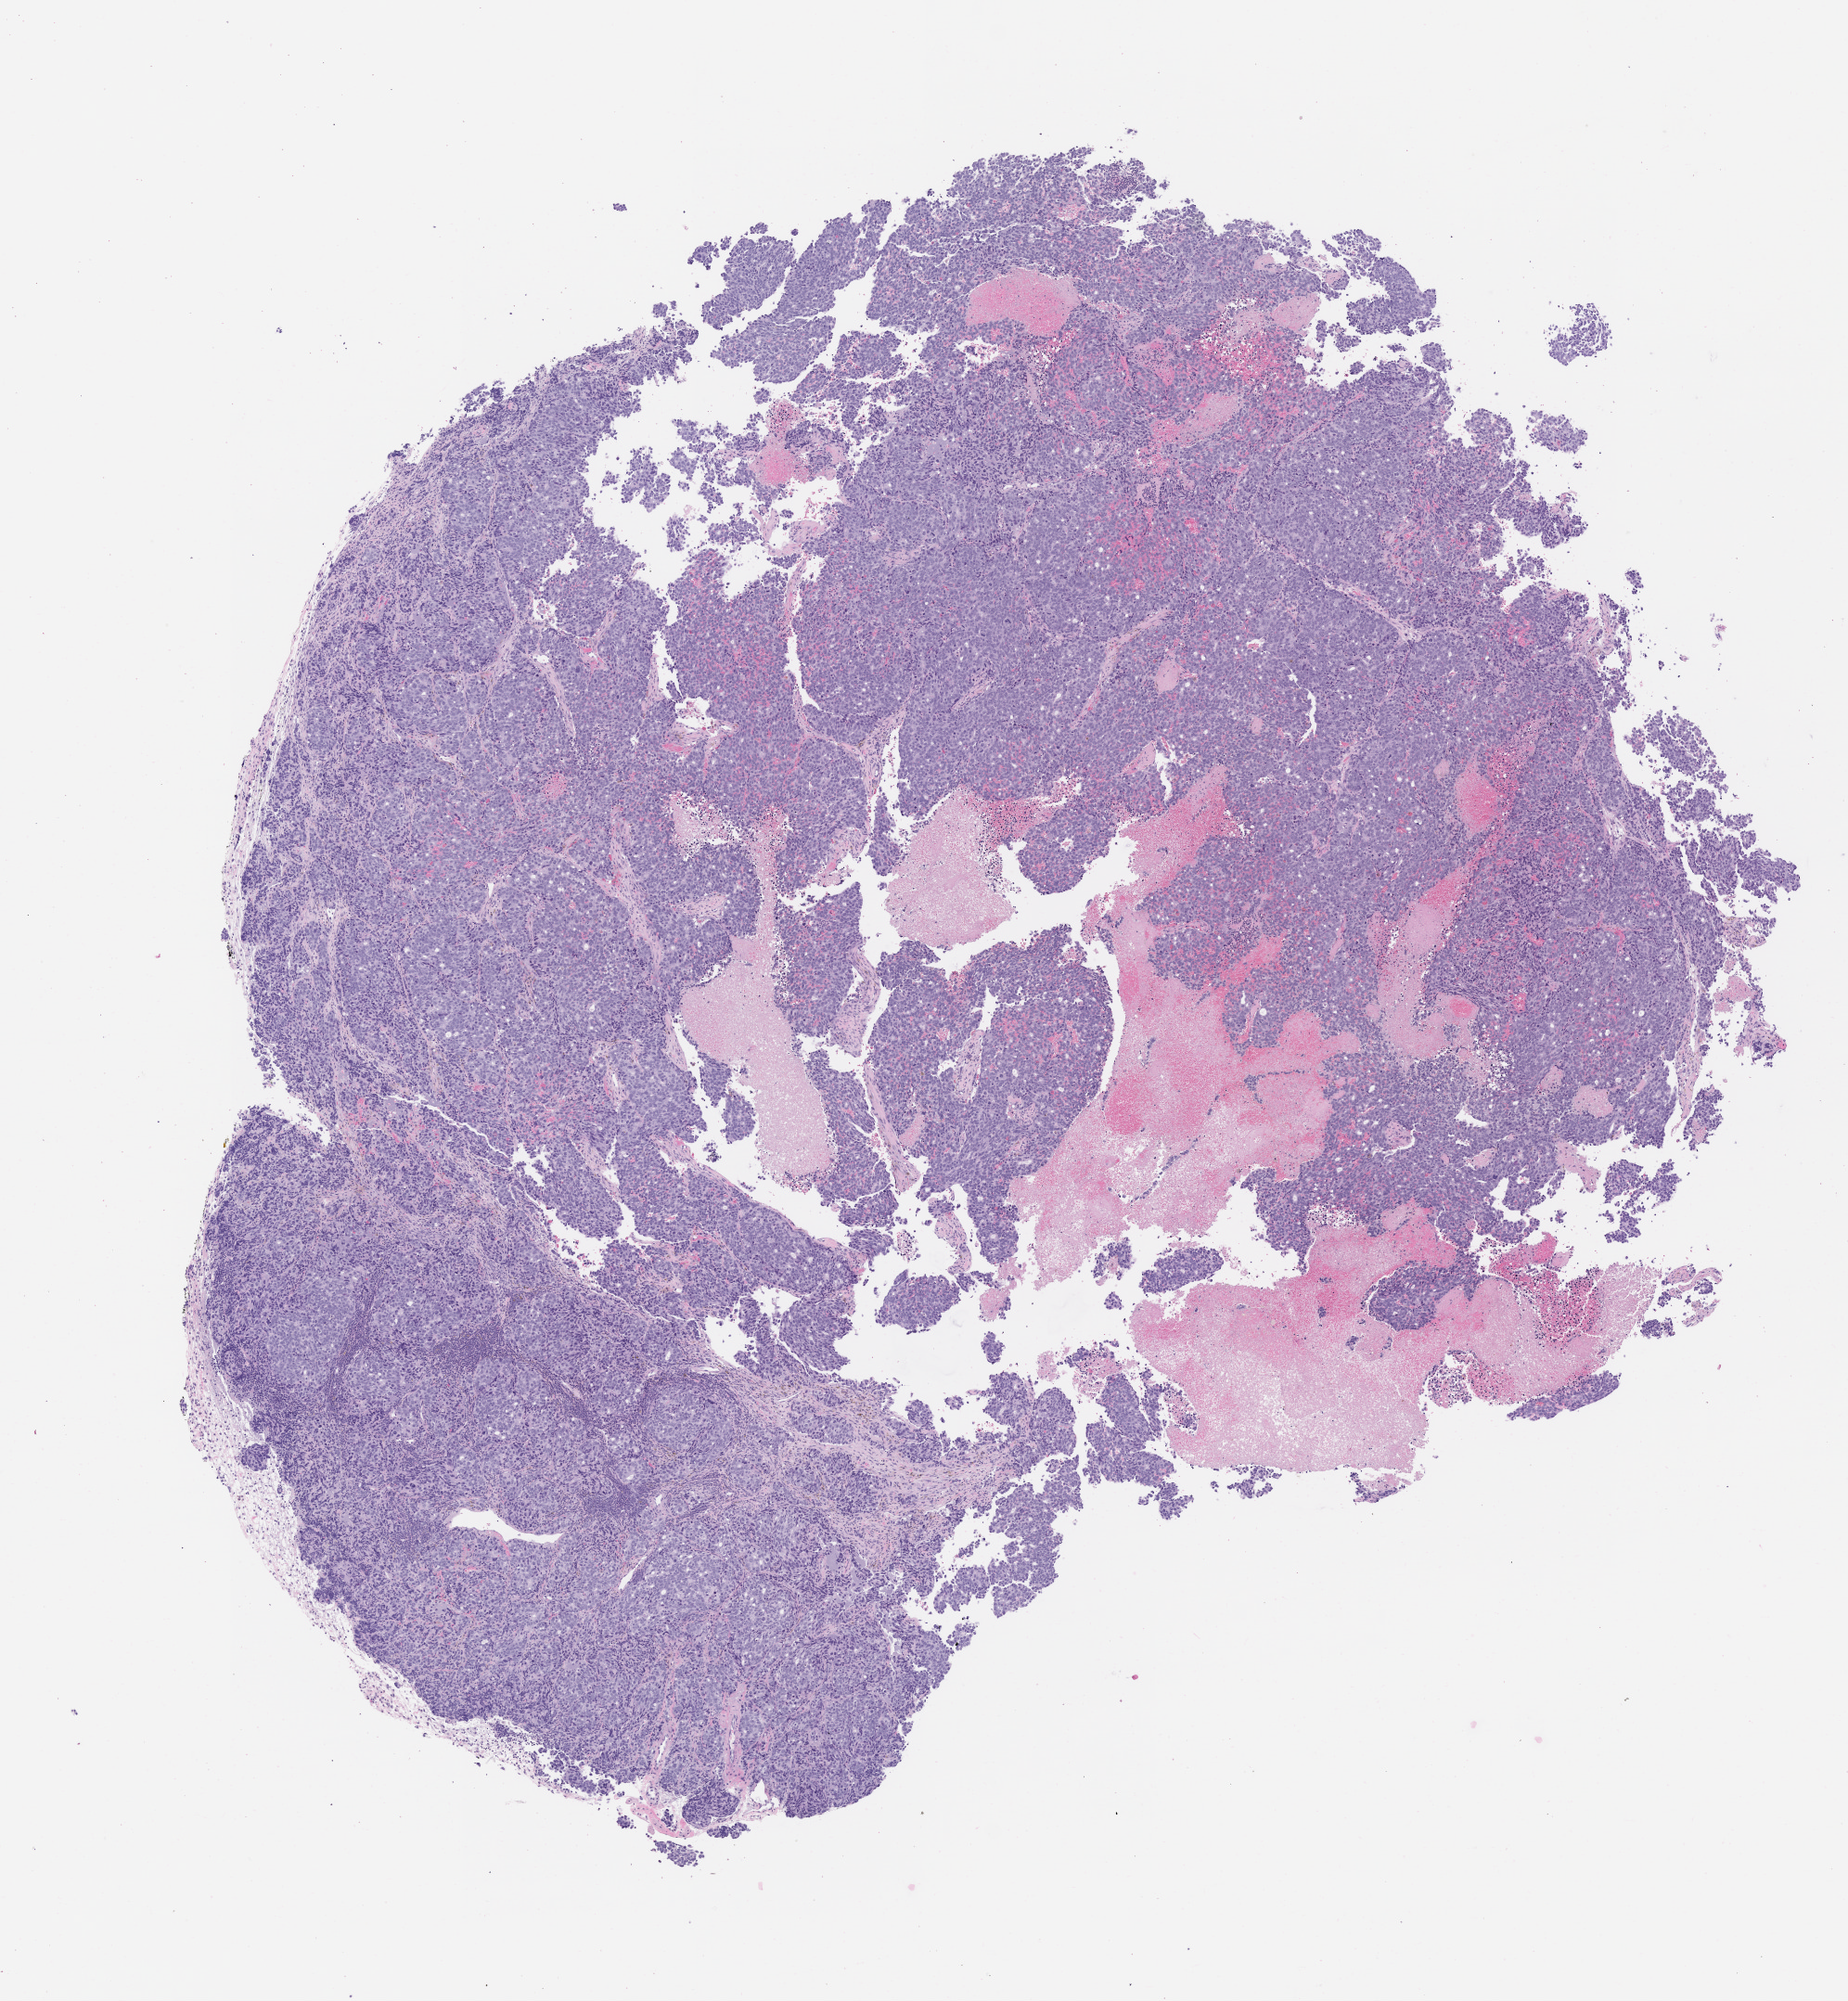
H&E whole-slide image of a patient-derived xenograft (PDX) tumor grown in a mouse, low-resolution overview of the scanned area, about 8.0 x 8.7 mm. Formalin-fixed paraffin-embedded section. Tumor site category: prostate.
Originating patient diagnosis: Prostate Carcinoma.